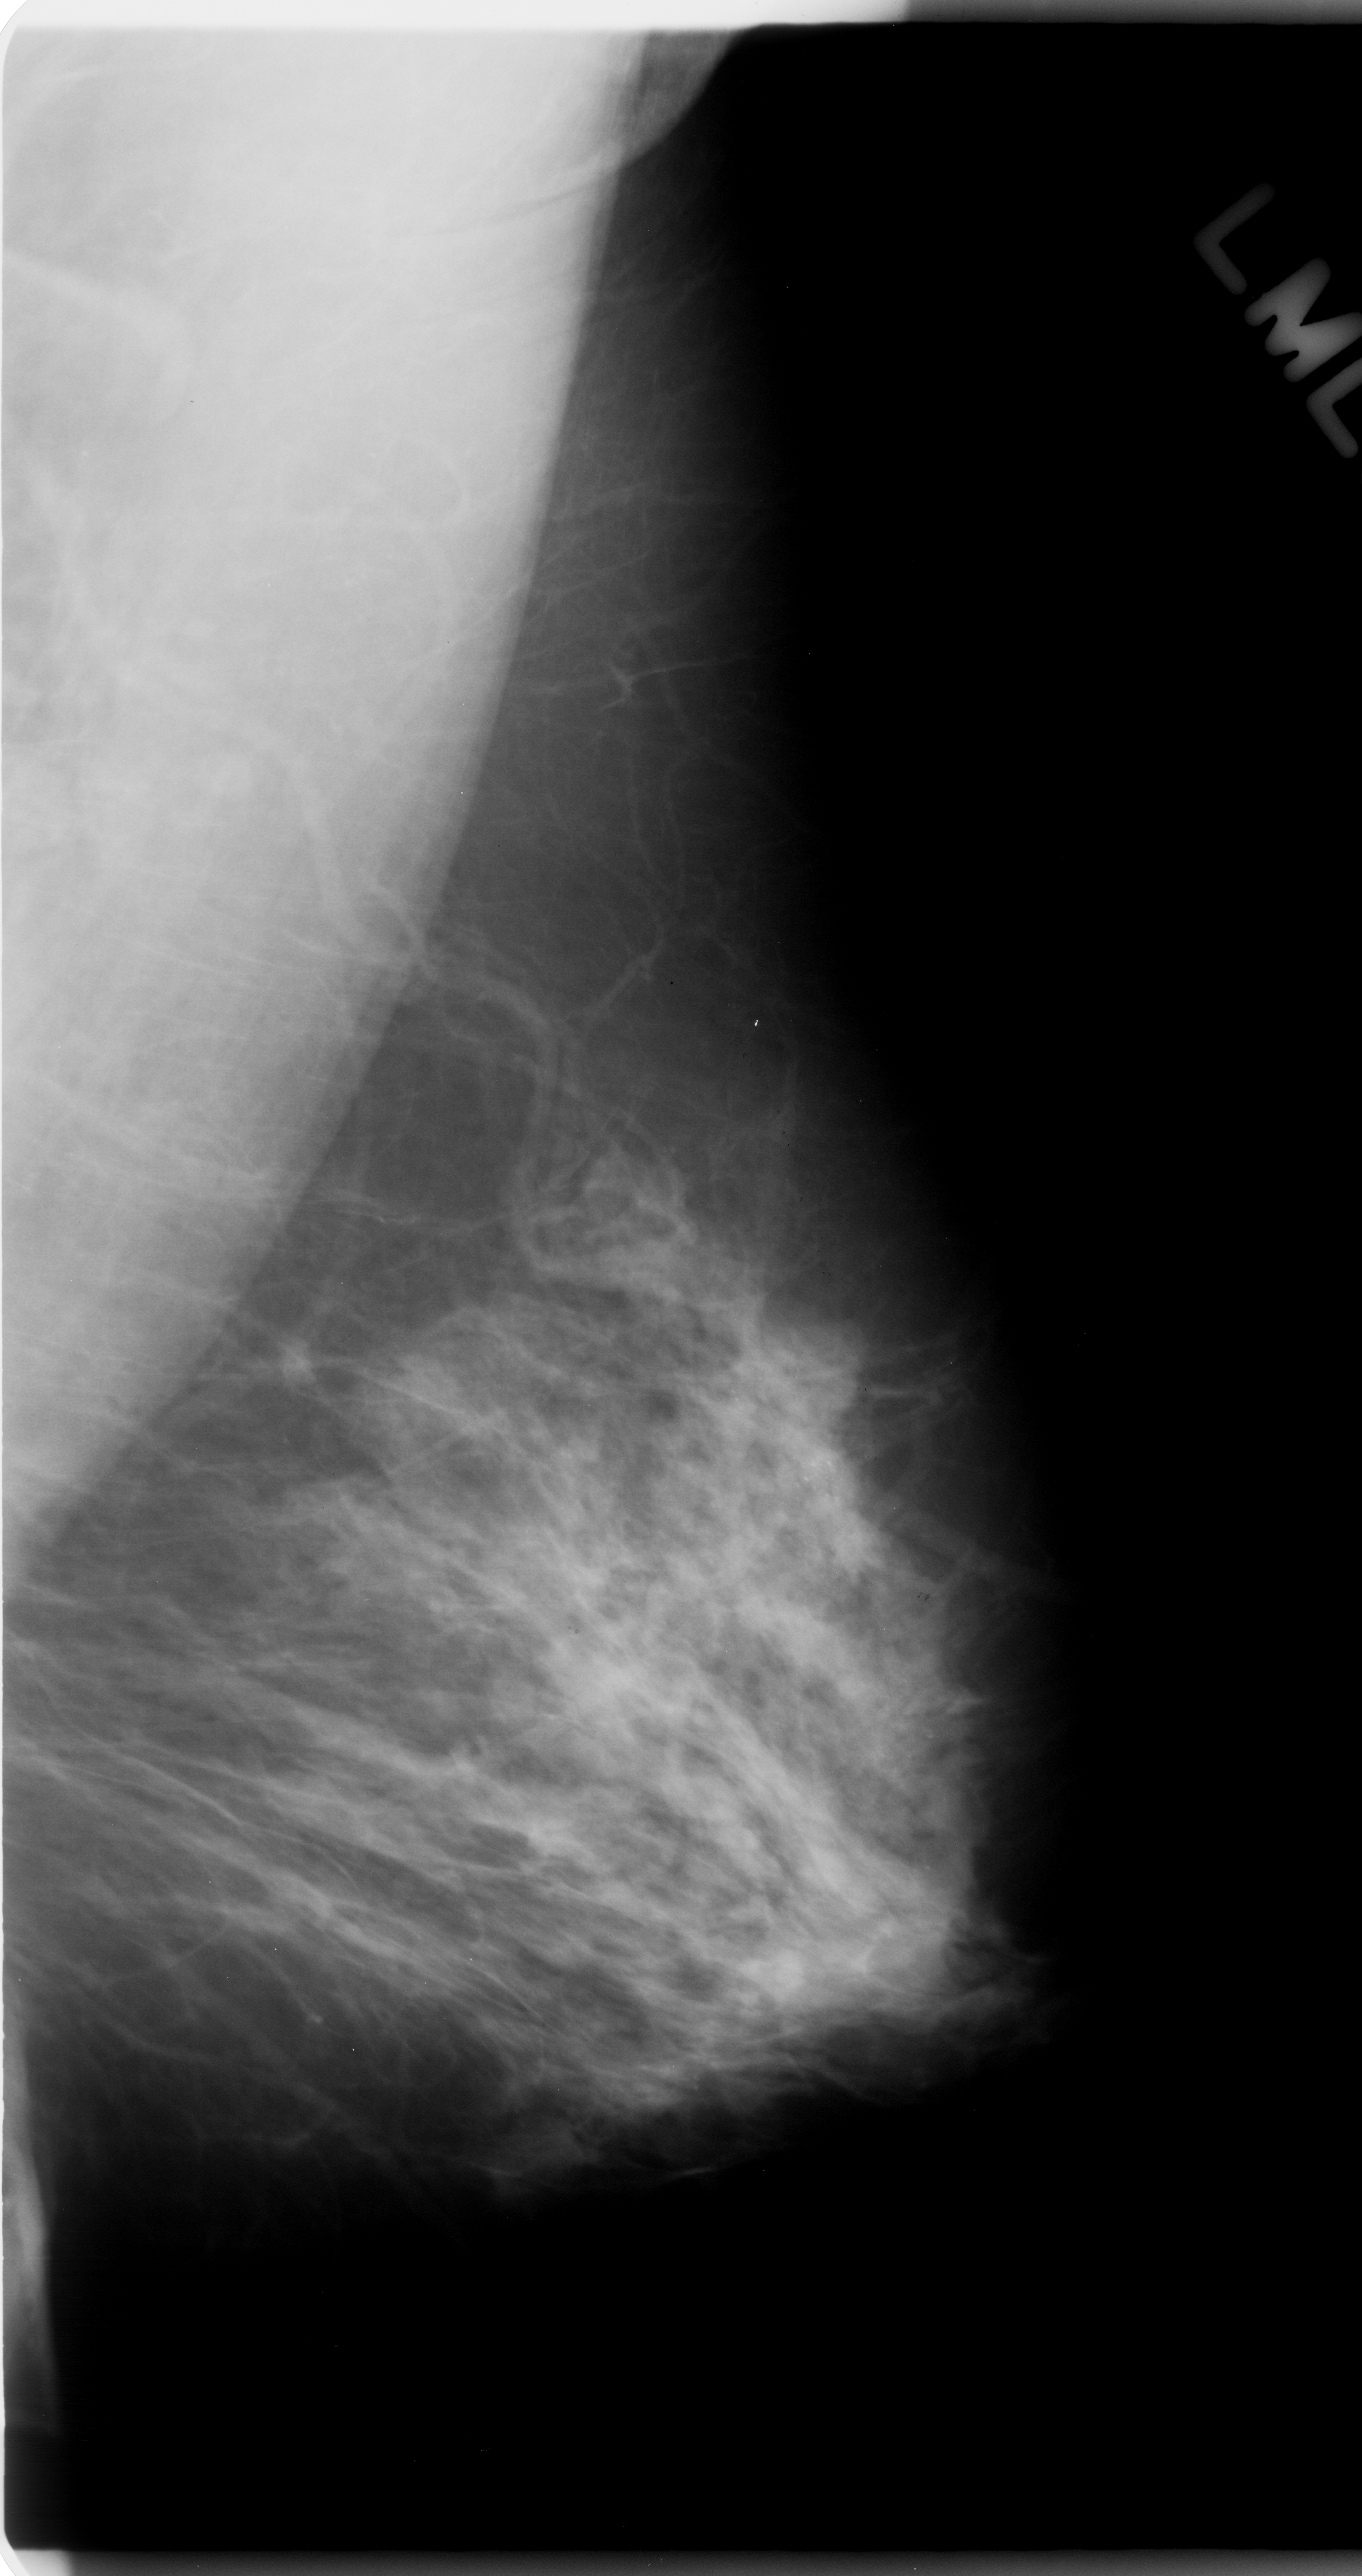
Scanned film-screen mammogram, left breast, MLO view, breast composition: scattered fibroglandular densities (BI-RADS density category 2 of 4).
- Radiologist-marked abnormalities on this image: calcifications, morphology amorphous, distribution regional; BI-RADS assessment category 4; subtlety rating 3 on a 1 (subtle) to 5 (obvious) scale; pathology result (as recorded, not read from the image): malignant.